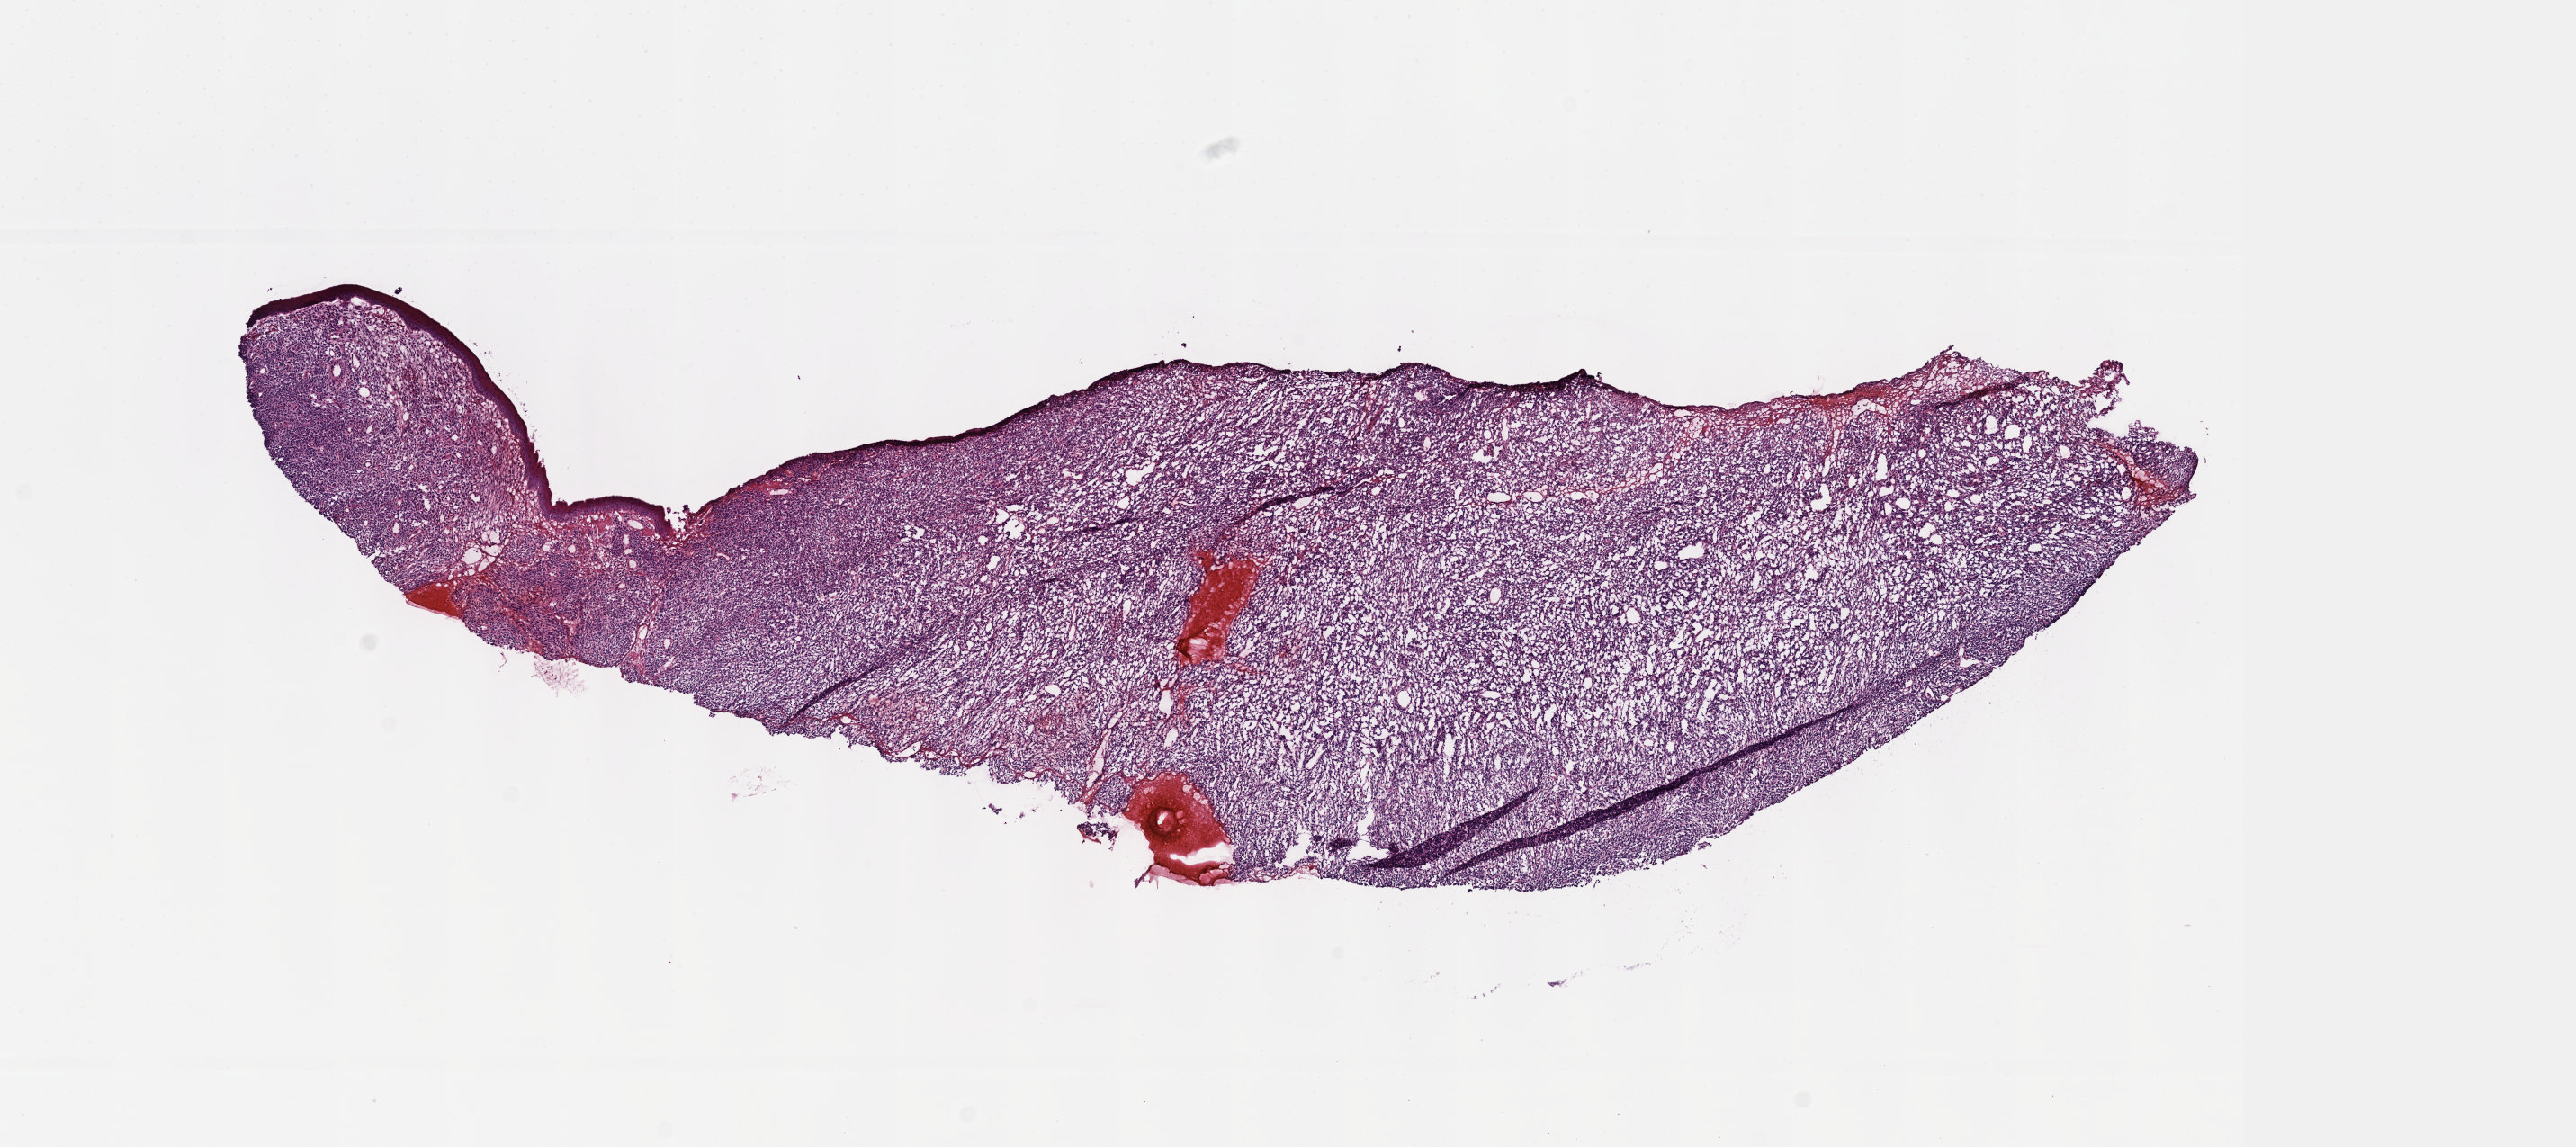
Digitized Hematoxylin and eosin (H&E) stained tissue section (whole slide), low-resolution overview of the scanned area, about 11.6 x 5.2 mm (slide scanned at 40x), frozen section from the top of the tissue portion, connective, subcutaneous and other soft tissues, primary tumour sample. Male patient; age at initial diagnosis 28 years. Pathologist review of this section (percent, as recorded): tumour cells 100%, tumour nuclei 80%, normal cells 0%, stromal cells 0%, necrosis 0%. Infiltration values recorded for this section: lymphocyte infiltration 1%, monocyte infiltration 0%, neutrophil infiltration 0%.
• pathologic diagnosis: Synovial sarcoma, spindle cell (connective, subcutaneous and other soft tissues of head, face, and neck)